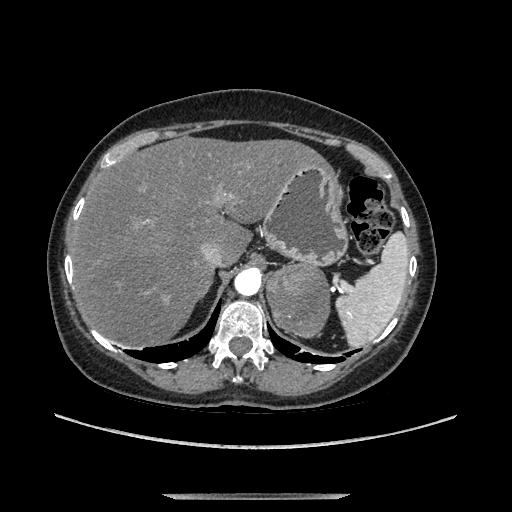
Contrast-enhanced abdominal CT, one axial slice; slice 99 of 169 in the series (ordered by position); soft-tissue window (W 400 / L 40 HU); 1.25 mm slice thickness; 512 × 512 image matrix, field of view 400 × 400 mm. Female patient. Case-level facts recorded for this patient, not image findings: diagnosis: adrenocortical carcinoma; tumour side: left adrenal; tumour size at pathology: 9 cm; Ki-67 index: 2 %; stage (as recorded): 3.
Outlined on this slice (semi-automatic segmentation, software-assisted and operator-edited):
- mass: box from (x=270, y=268) to (x=328, y=335) px